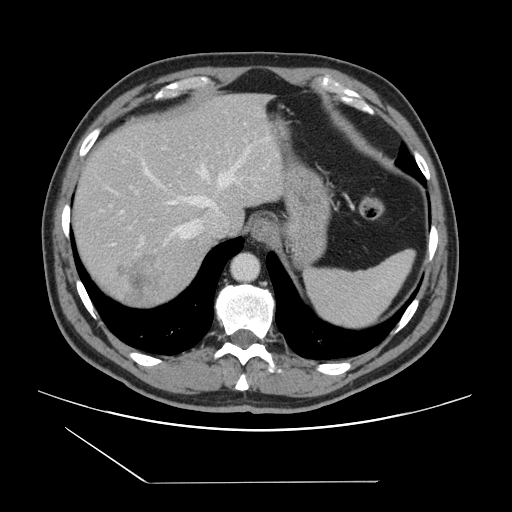
Contrast-enhanced abdominal CT, one axial slice. Slice 119 of 157 in the series (ordered by position). Intravenous contrast given. Soft-tissue window (W 400 / L 40 HU). 2.5 mm slice thickness. 512 × 512 image matrix, field of view 407 × 407 mm. Male patient, age 61 years. Case-level facts recorded for this patient, not image findings: diagnosis: colorectal cancer liver metastases, imaged before liver resection.
Annotated regions visible in this slice (expert manual segmentation):
- hepatic veins: bounding box [x1, y1, x2, y2] px = [121, 150, 250, 245]
- liver: [72, 94, 284, 309]
- planned liver remnant (the part of the liver to remain after resection): [73, 95, 235, 232]
- portal vein (with intrahepatic branches): [129, 186, 143, 245]
- liver metastasis: [116, 253, 170, 308]